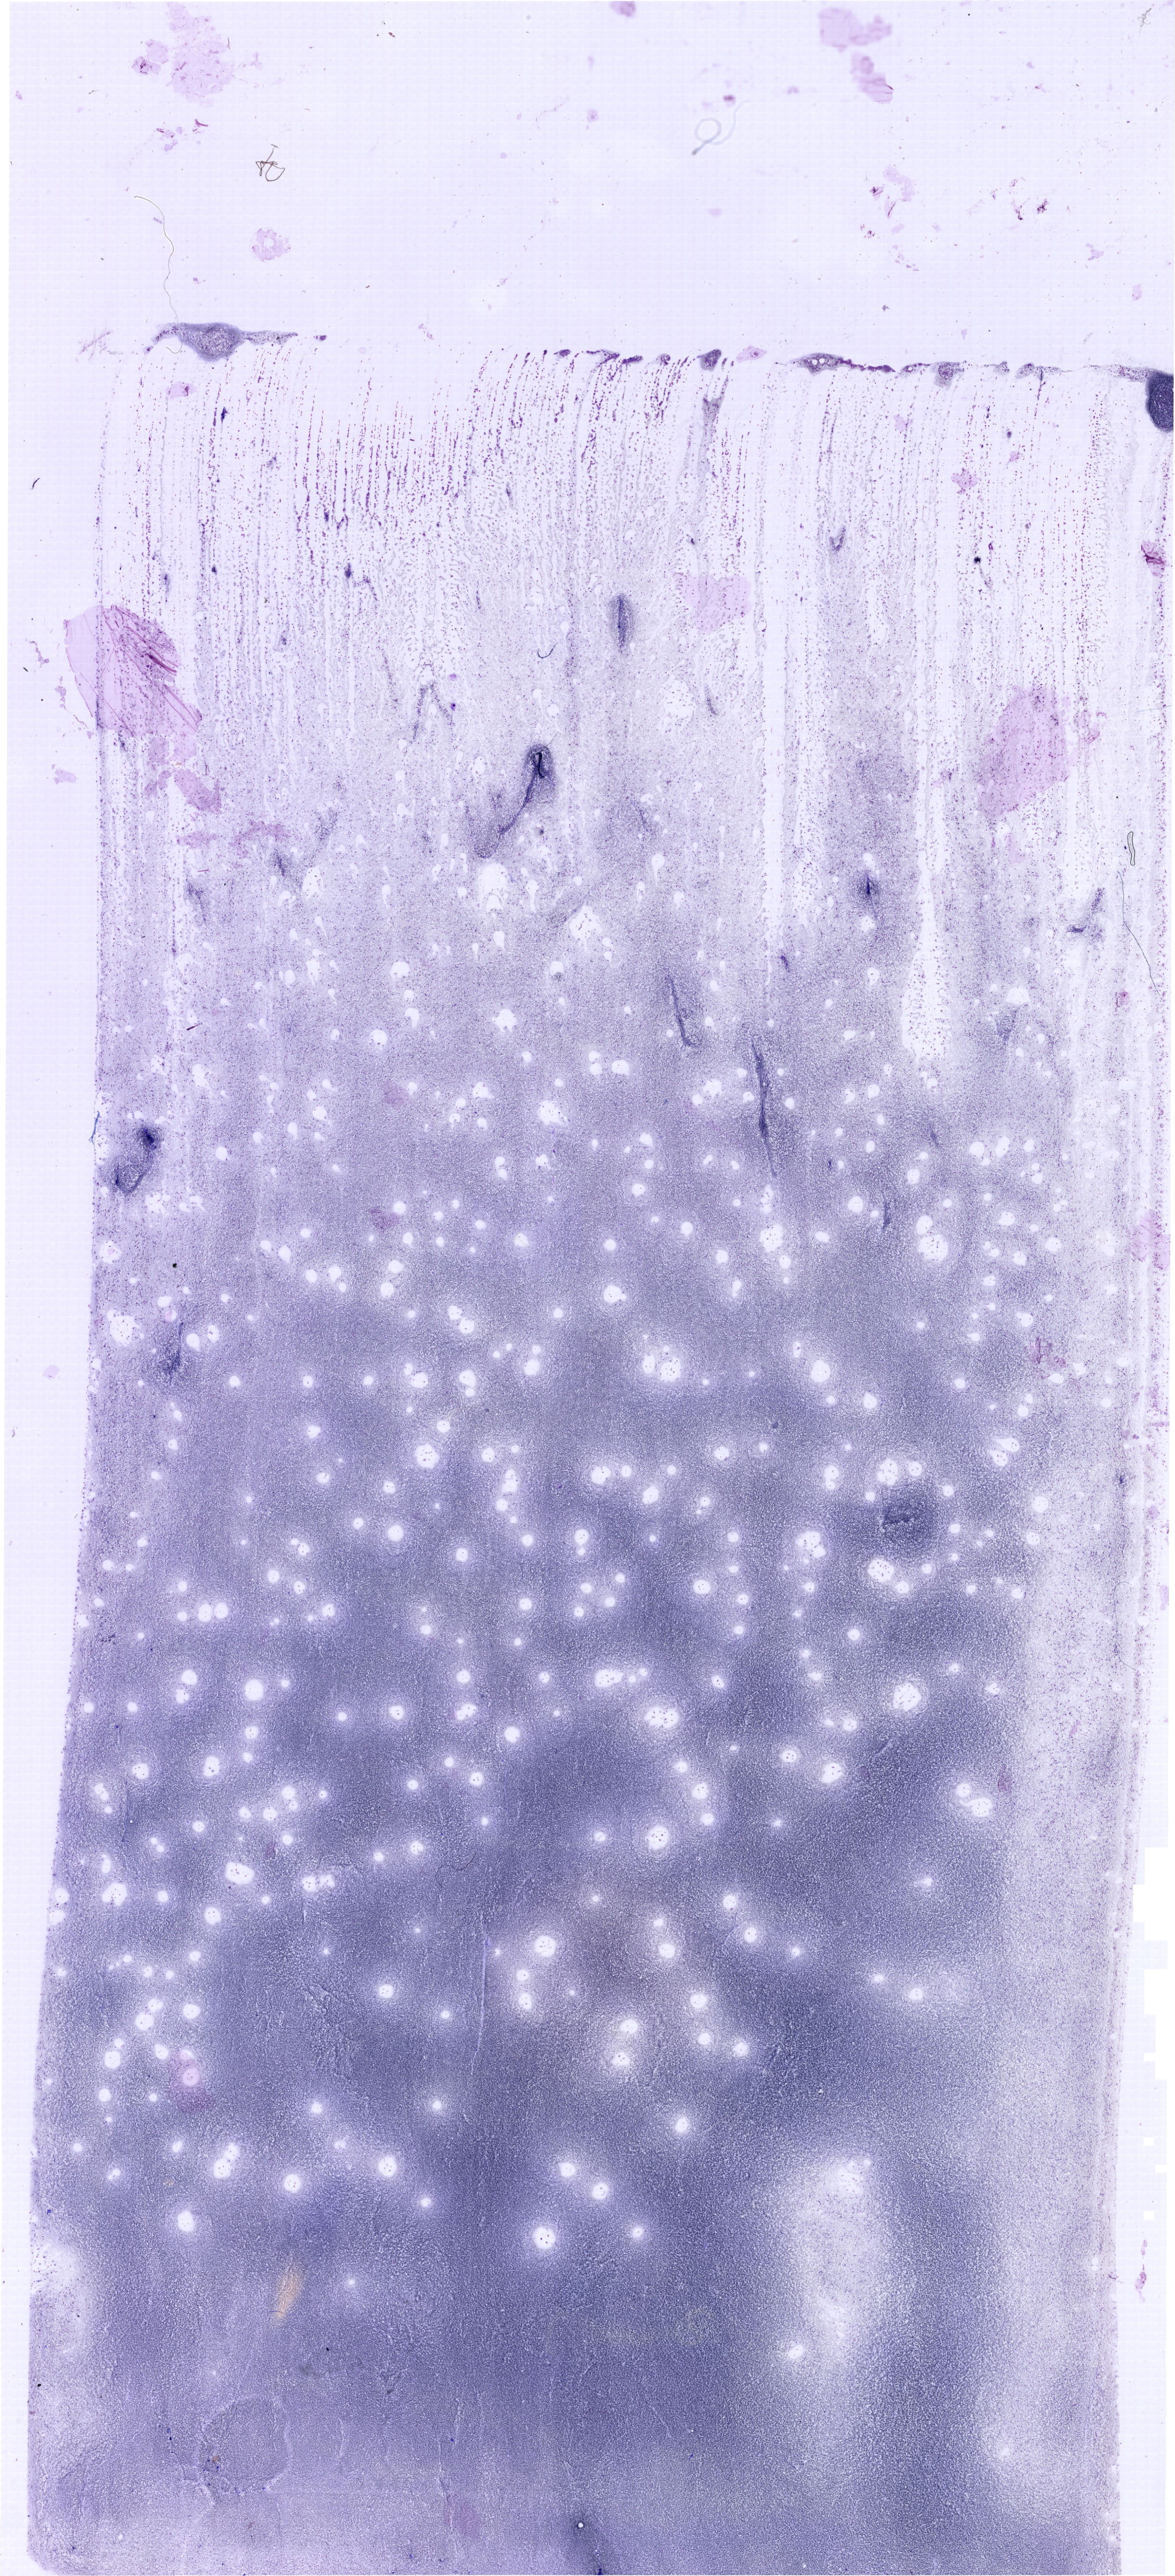
Whole-slide image of a May-Grünwald-Giemsa (MGG)-stained bone marrow aspirate smear, whole scanned area (about 19.7 x 43.2 mm) shown as a low-resolution overview. Female patient.
Diagnosis: Mixed Phenotype Acute Leukemia, B/Myeloid.